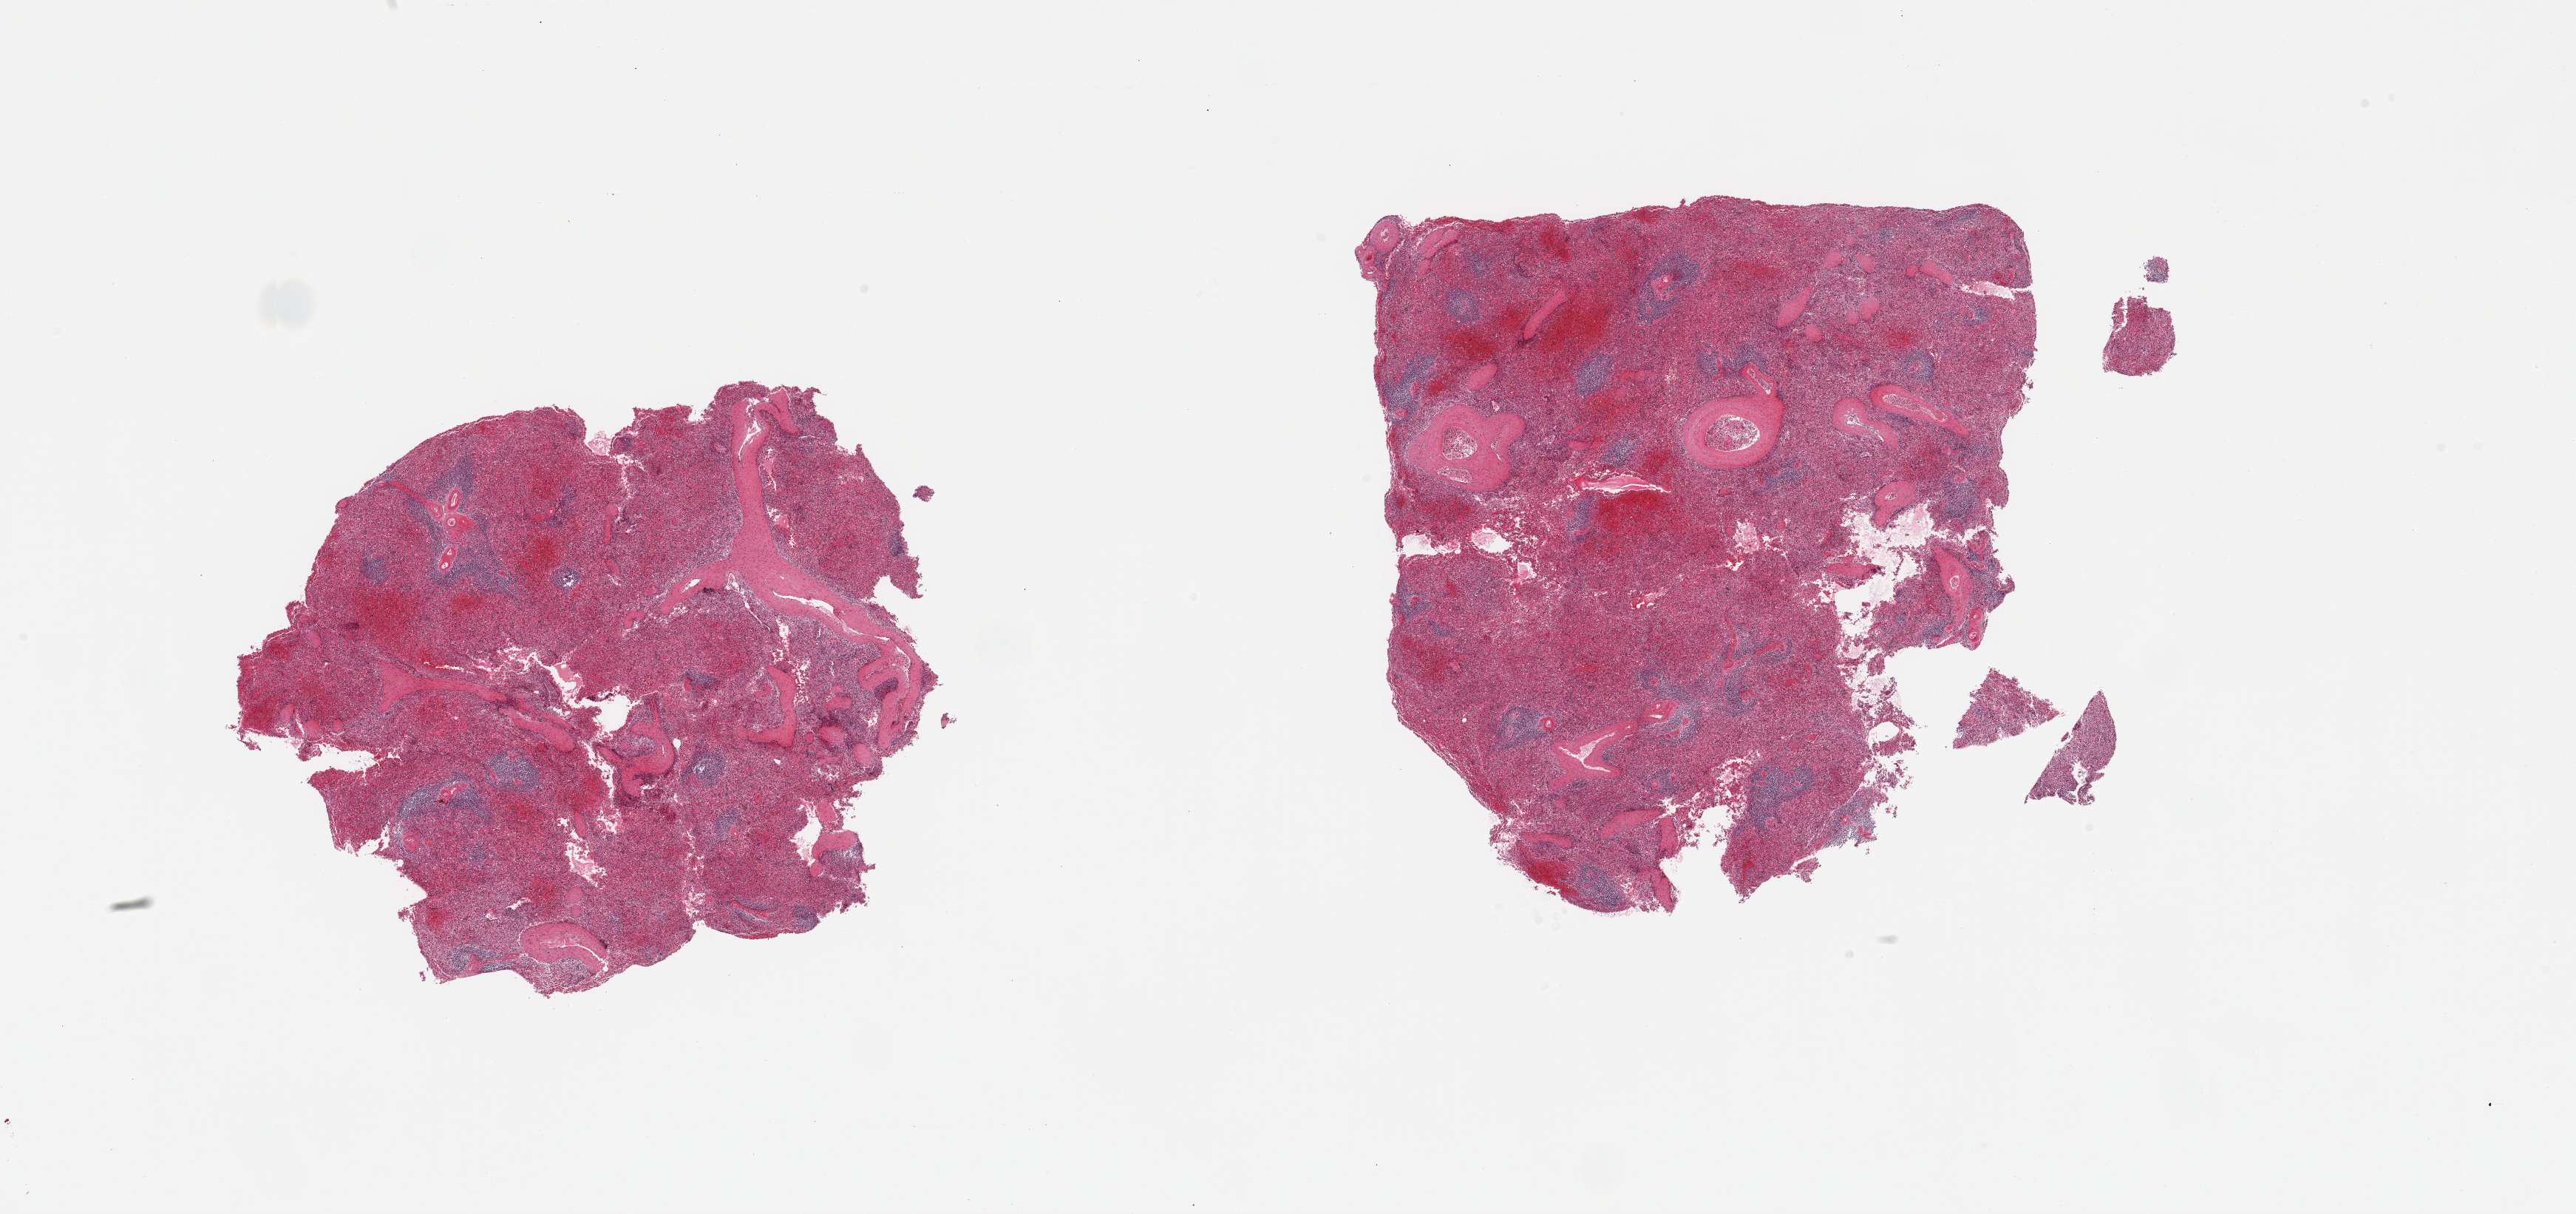
Whole-slide image, hematoxylin and eosin (H&E) stain — shown as a low-resolution overview of the whole scanned area (about 27.6 x 13.0 mm, slide scanned at 20x); PAXgene-fixed paraffin-embedded (PFPE) section; sampled site (target tissue): spleen; tissue donor sample. Donor sex: female.
Pathologist's review note for this sample: 2 pieces, moderate congestion.